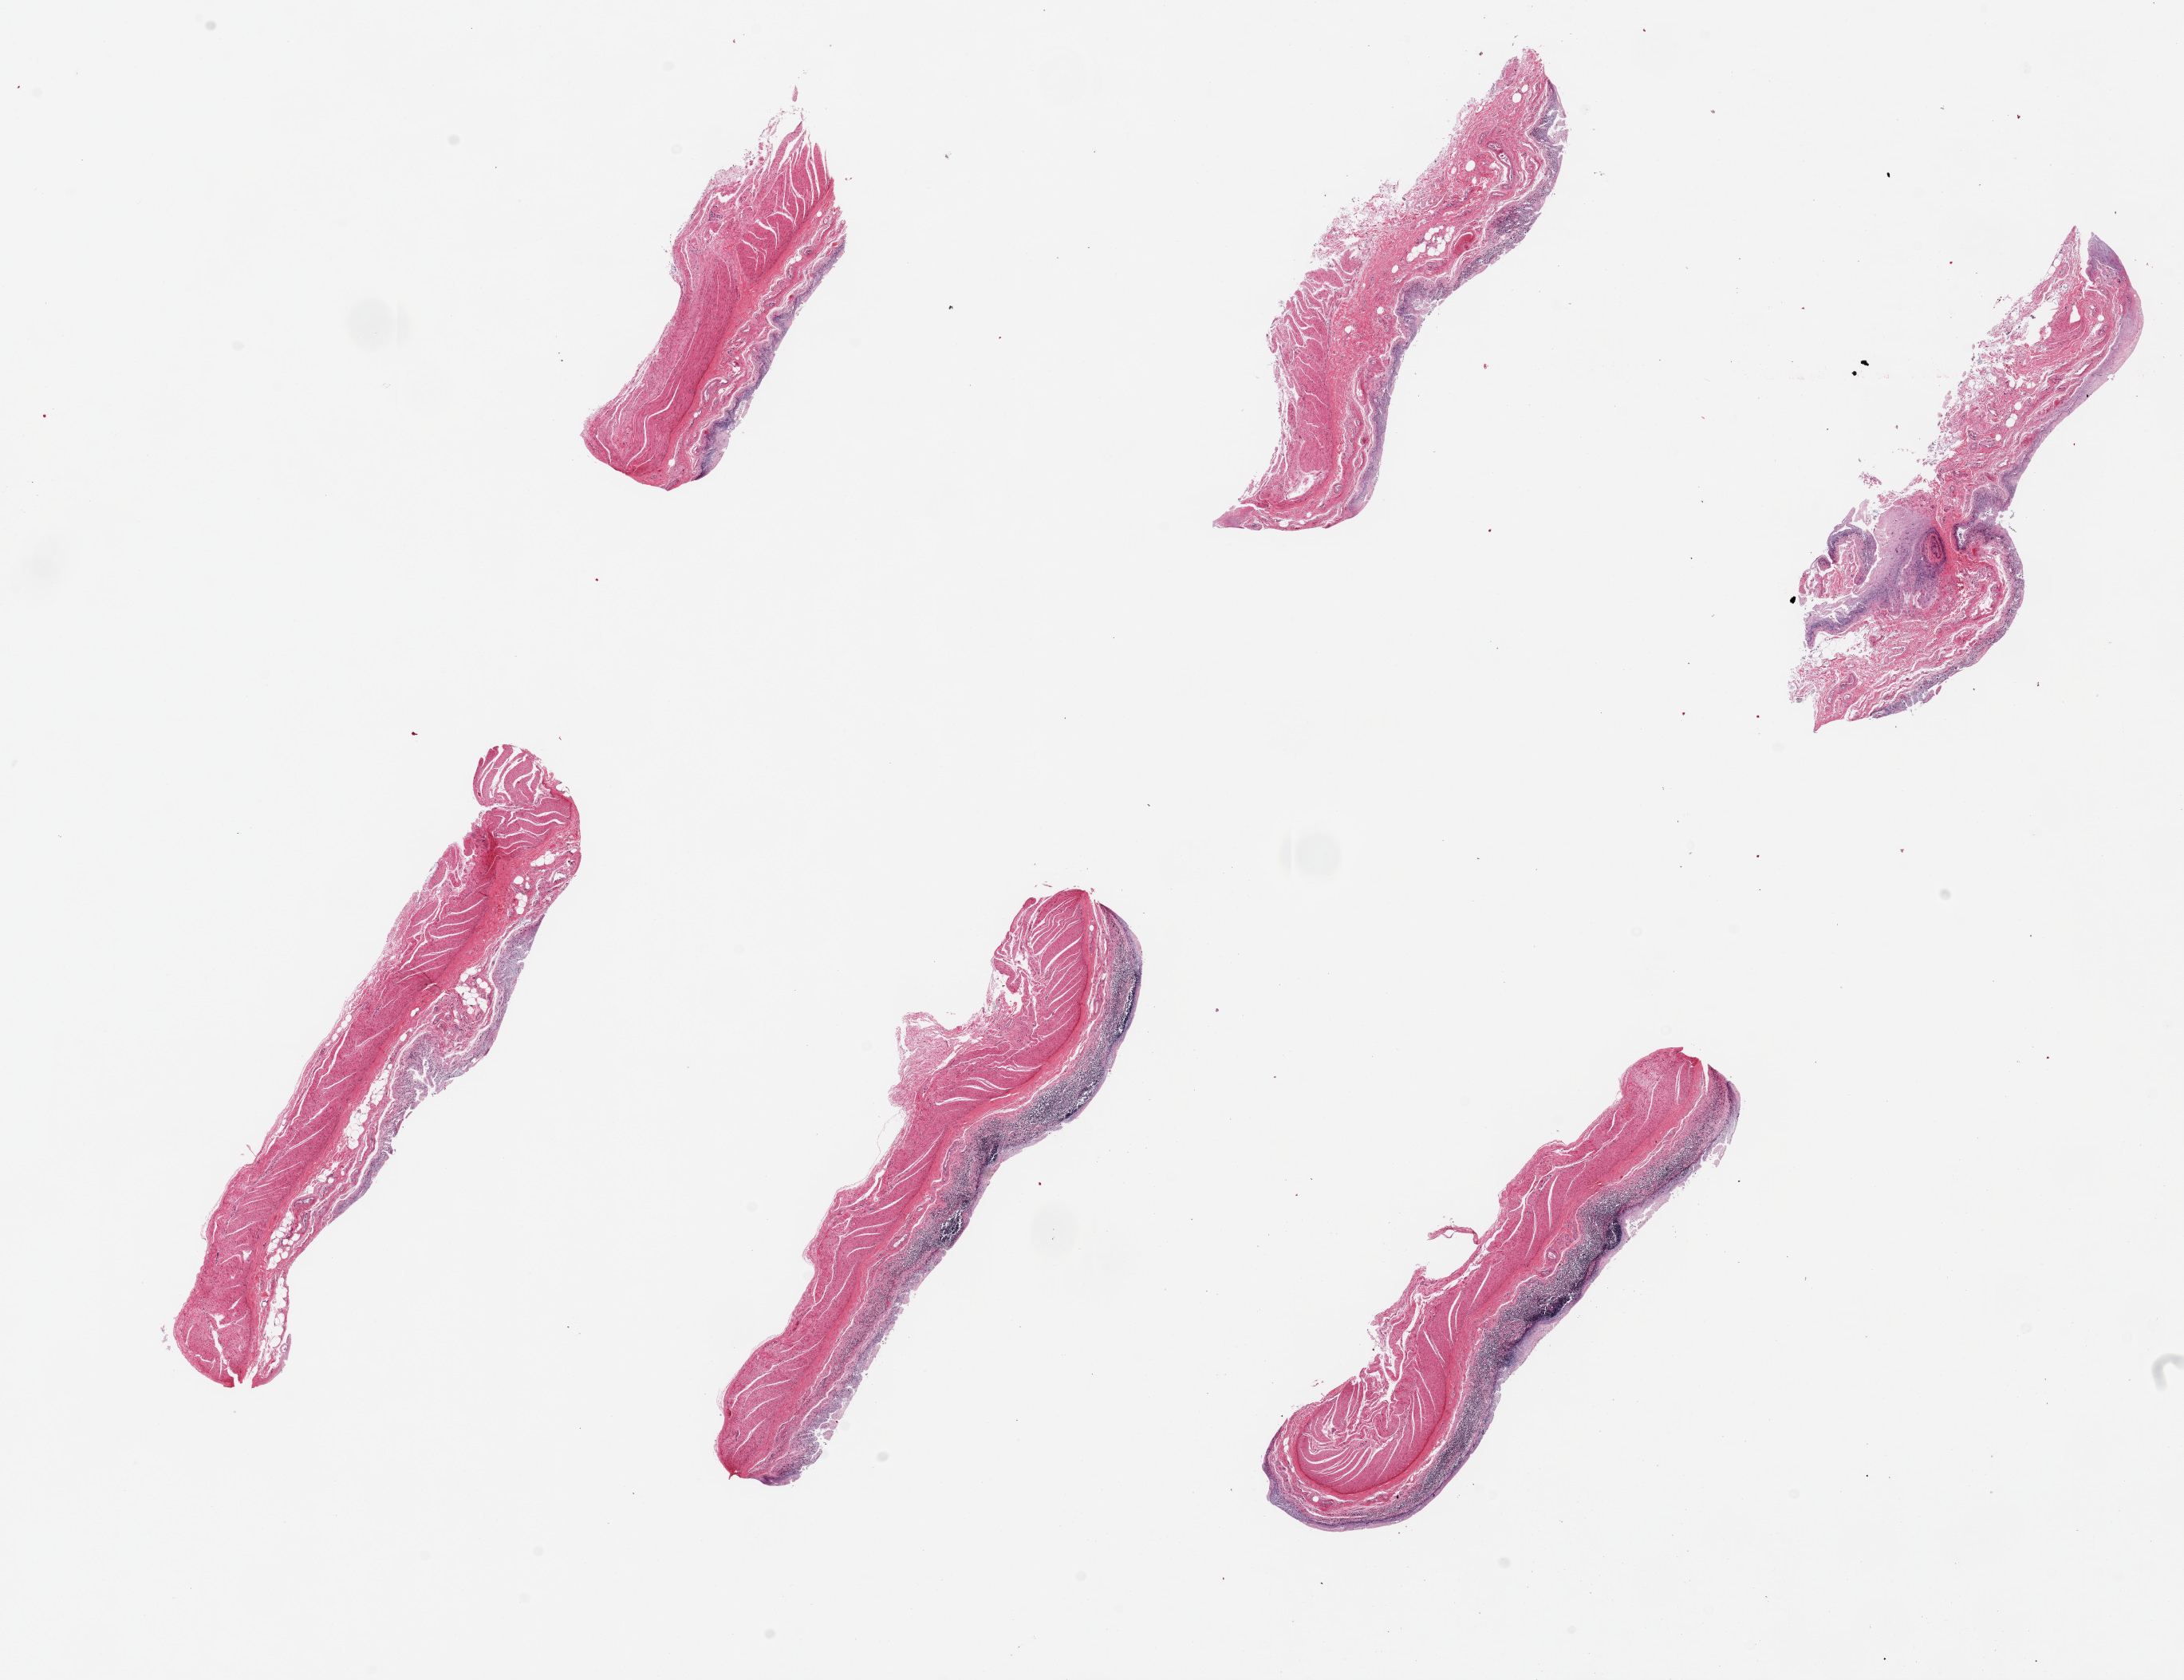
Digitized H&E-stained section, brightfield, shown as a low-resolution overview of the whole scanned area (about 21.7 x 16.7 mm); PAXgene-fixed, paraffin-embedded tissue; target tissue: ileum; donor tissue sample.
Pathologist's review note for this sample: 6 pieces, up to 7x1.5mm; mucosa totally autolyzed, but lymphoid tissue is present in submucosa of the two largest pieces; muscularis present.